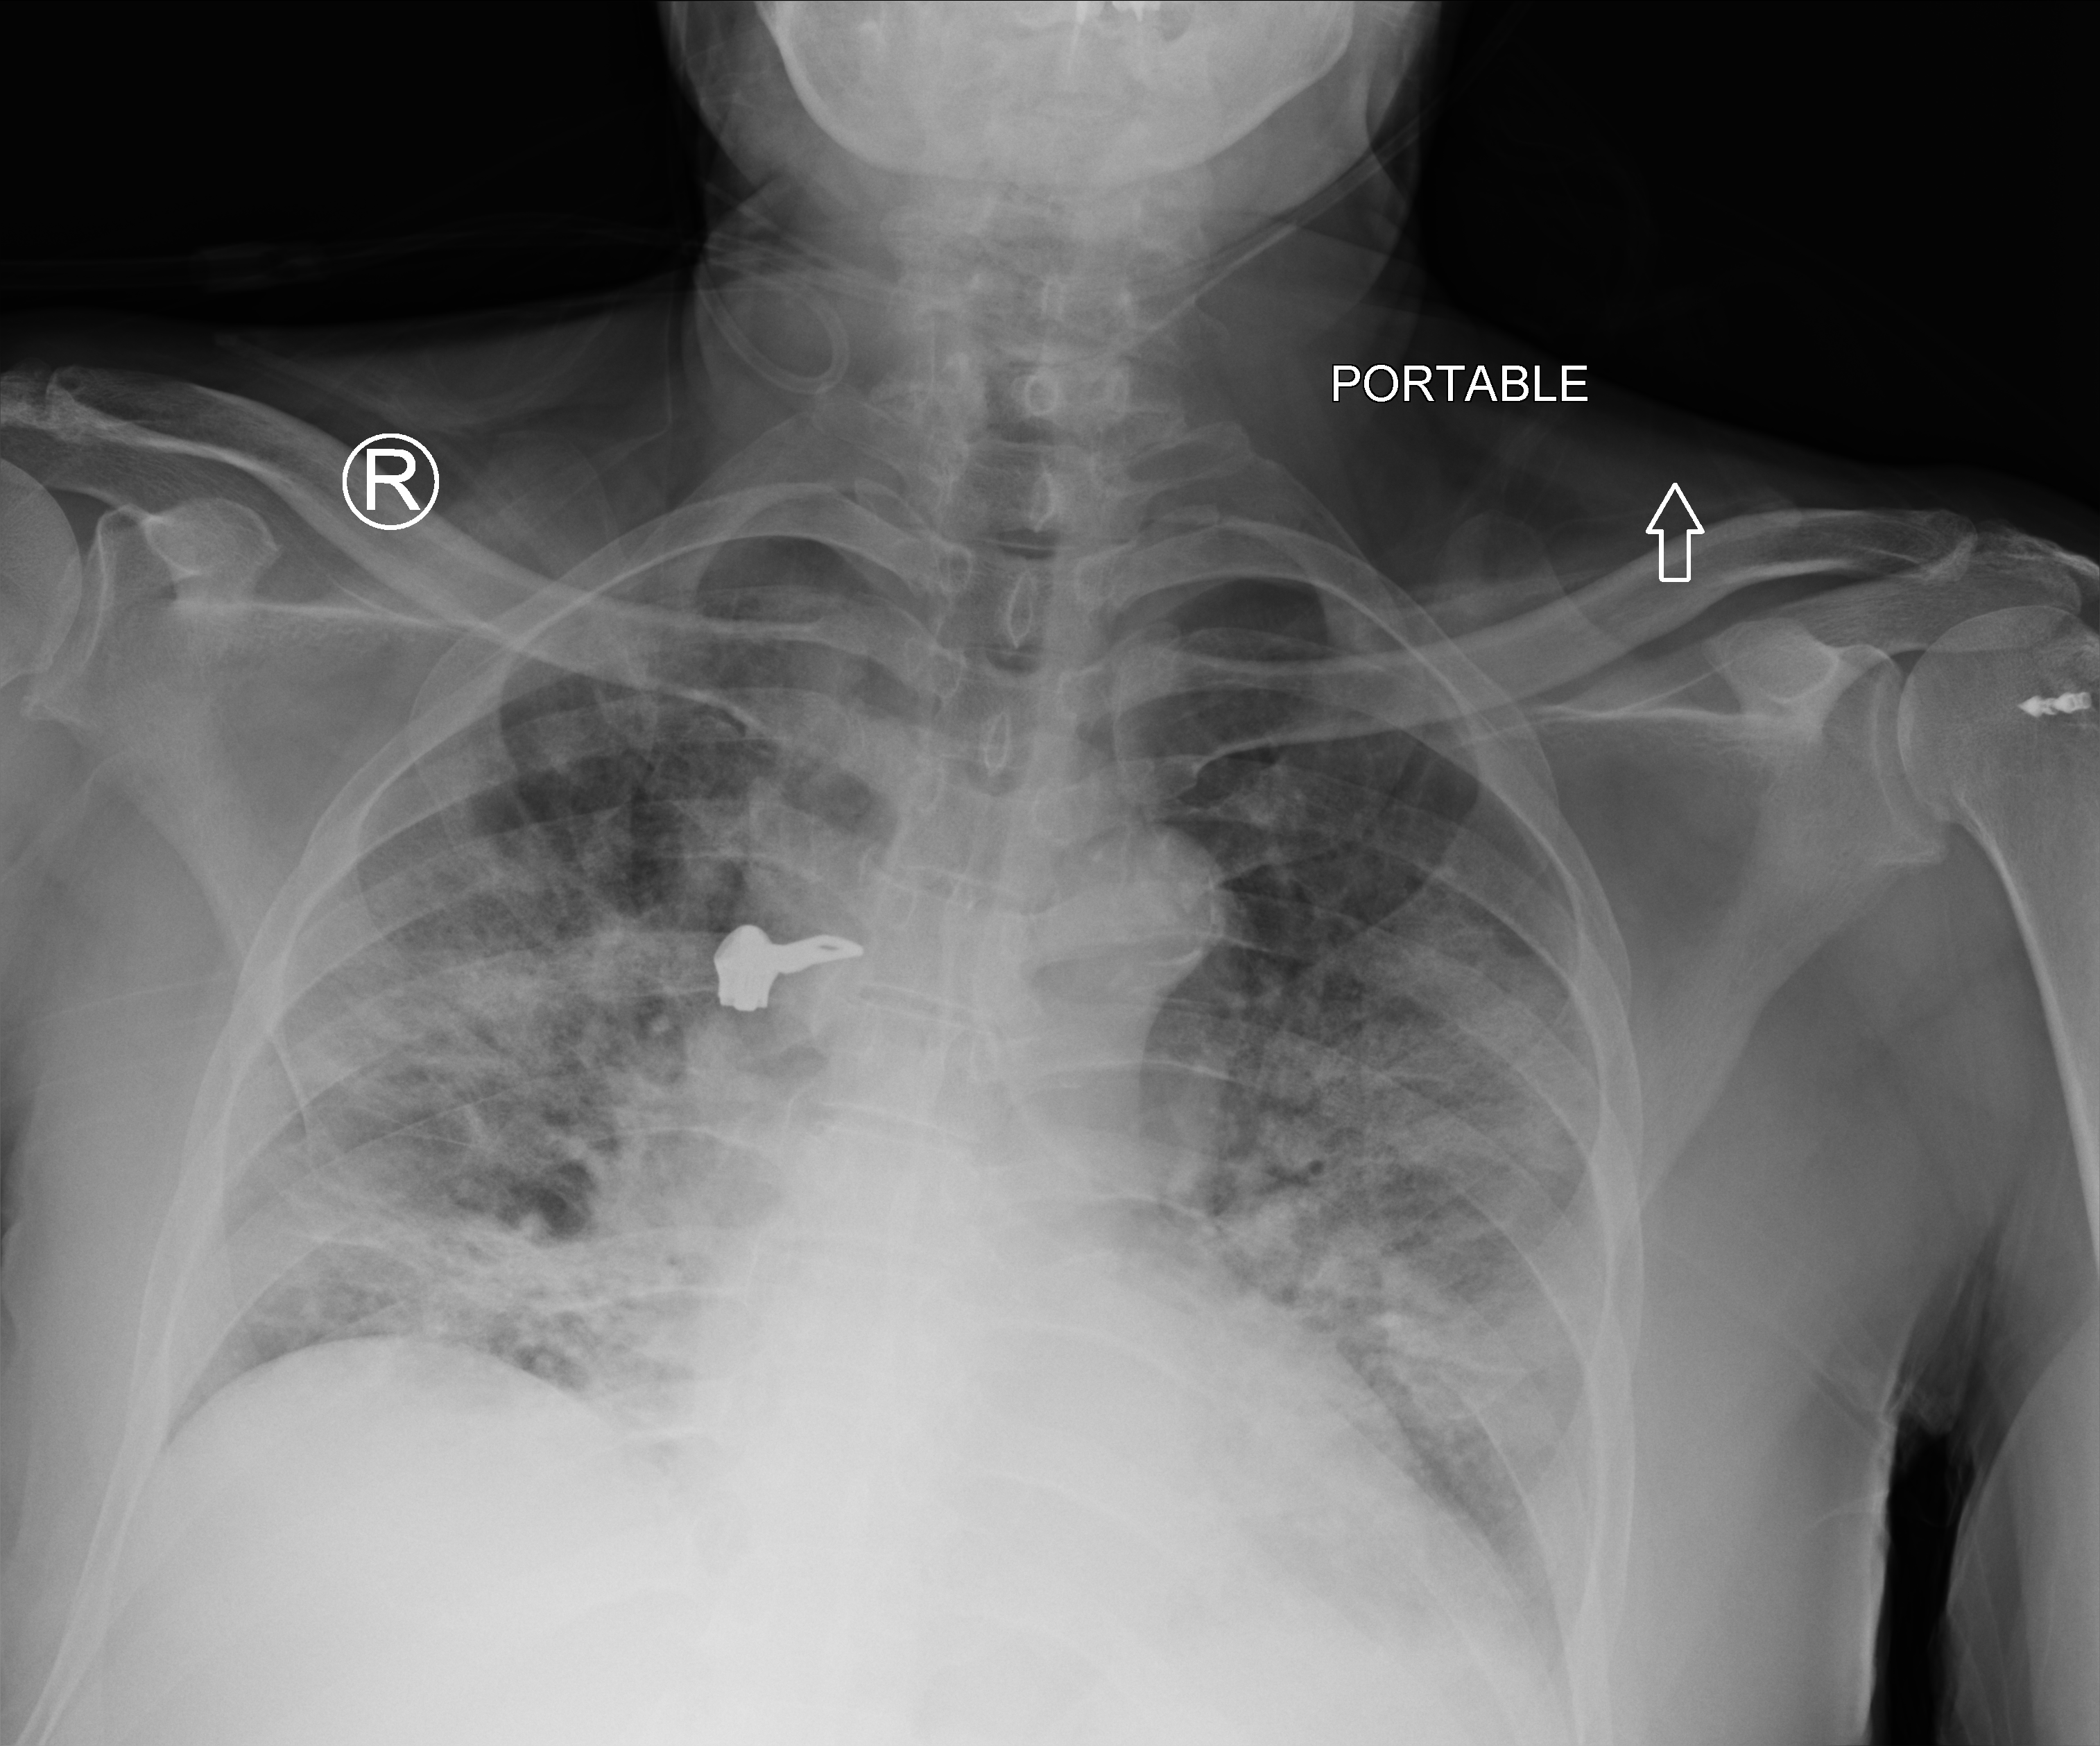
Portable chest radiograph, anteroposterior (AP) projection. Patient hospitalised with COVID-19; male, aged 60–74 years.
From the hospital-stay record, not from the radiograph (when in the stay this image was taken is not recorded):
- chronic kidney disease (admission record): no